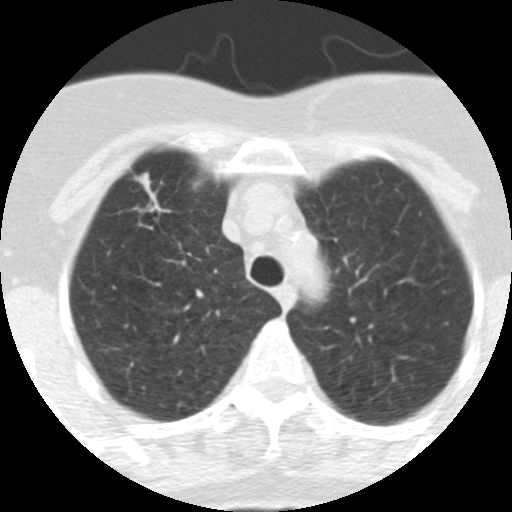
Low-dose screening chest CT, one axial slice. Position 250 of 313 along the scan axis. 120 kVp. Lung window (W 1500 / L -600 HU). 512 × 512 image matrix, field of view 253 × 253 mm.
Structures marked on this image (manually delineated by an expert):
- lesion 1 (tumor, upper lobe of right lung): bounding box [x1, y1, x2, y2] px = [134, 173, 163, 212]